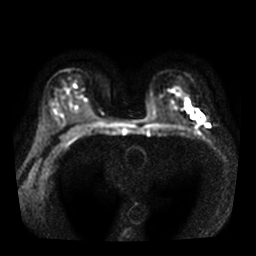
Breast MRI, one axial slice. Position 22 of 36 along the scan axis. Diffusion-weighted series; image 2 of 4 stored at this slice position (different b-values; order by instance number). 3 T. 5 mm slice thickness. 256 × 256 image matrix, field of view 320 × 320 mm. Female patient.
Annotated regions visible in this slice (manually delineated by an expert):
- tumour on diffusion-weighted imaging: bounding box (x1, y1, x2, y2) in pixels: (187, 106, 203, 121)